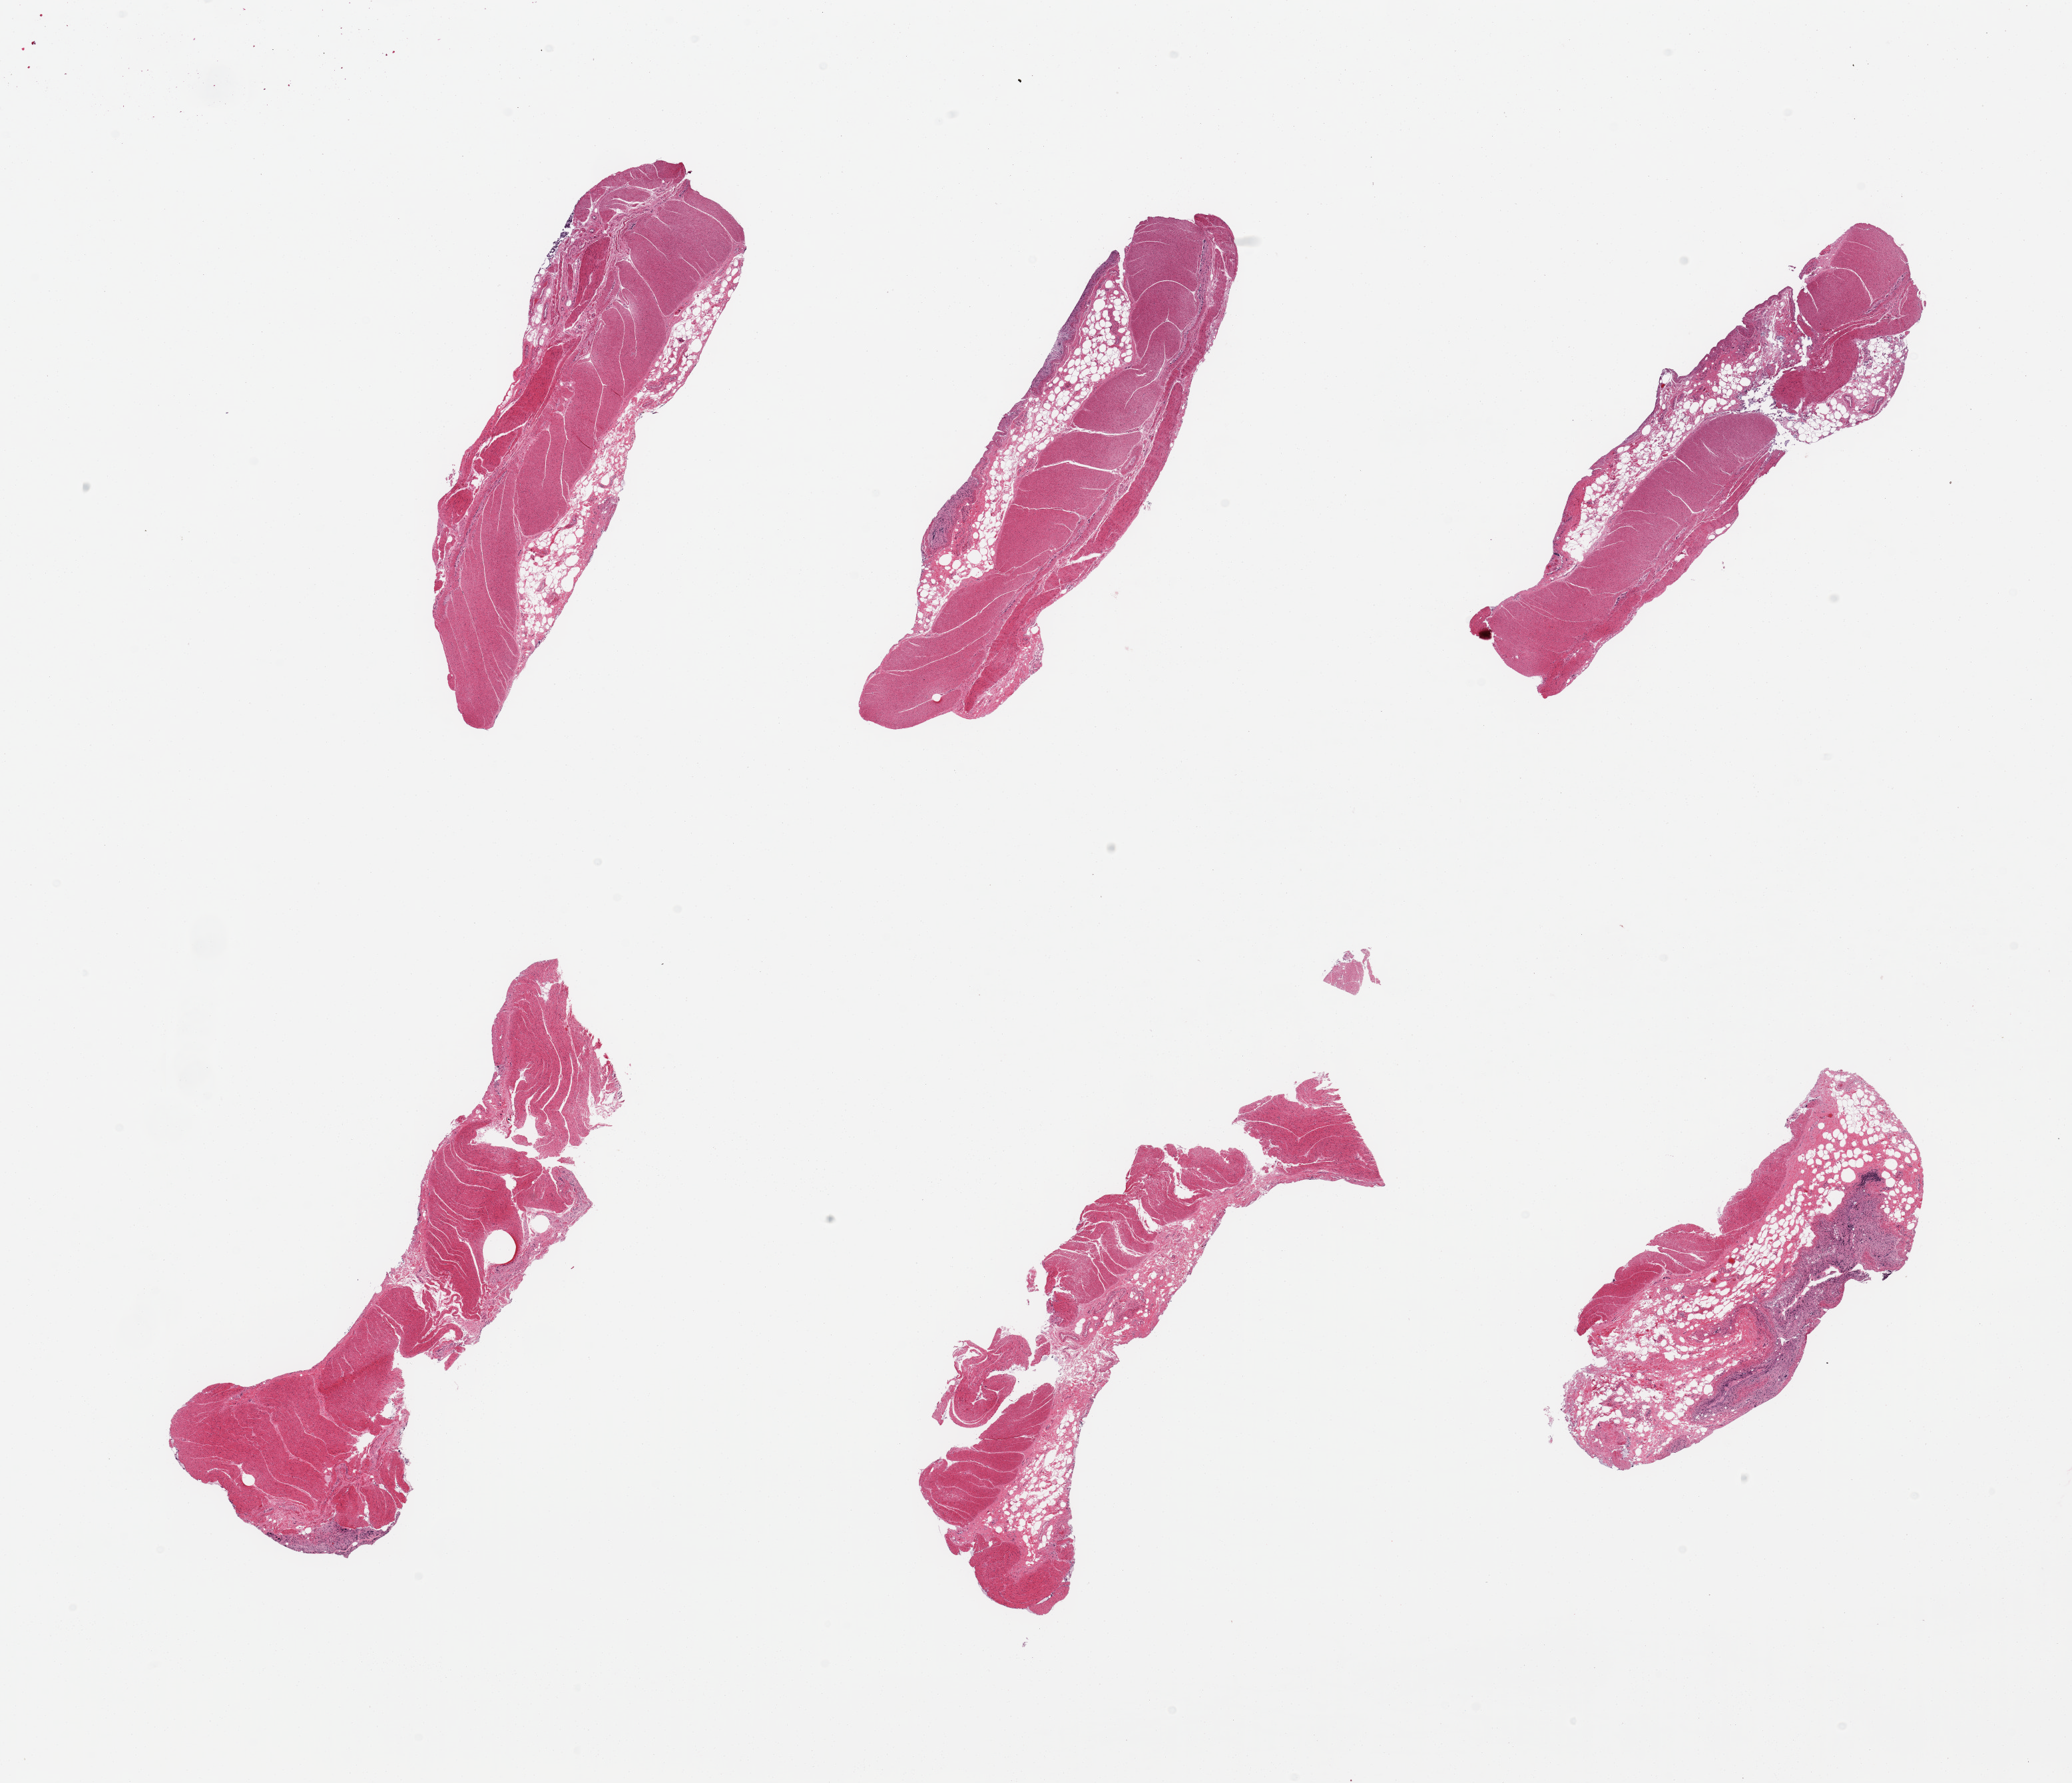
Digitized hematoxylin and eosin (H&E)-stained section — whole scanned area (about 24.6 x 21.2 mm) shown as a low-resolution overview; PAXgene-fixed paraffin-embedded (PFPE) section; target tissue: sigmoid colon; donor tissue sample. Male donor.
• pathologist's review note for this sample: 6 pieces; totally autolyzed mucosal remnants and preserved target muscularis